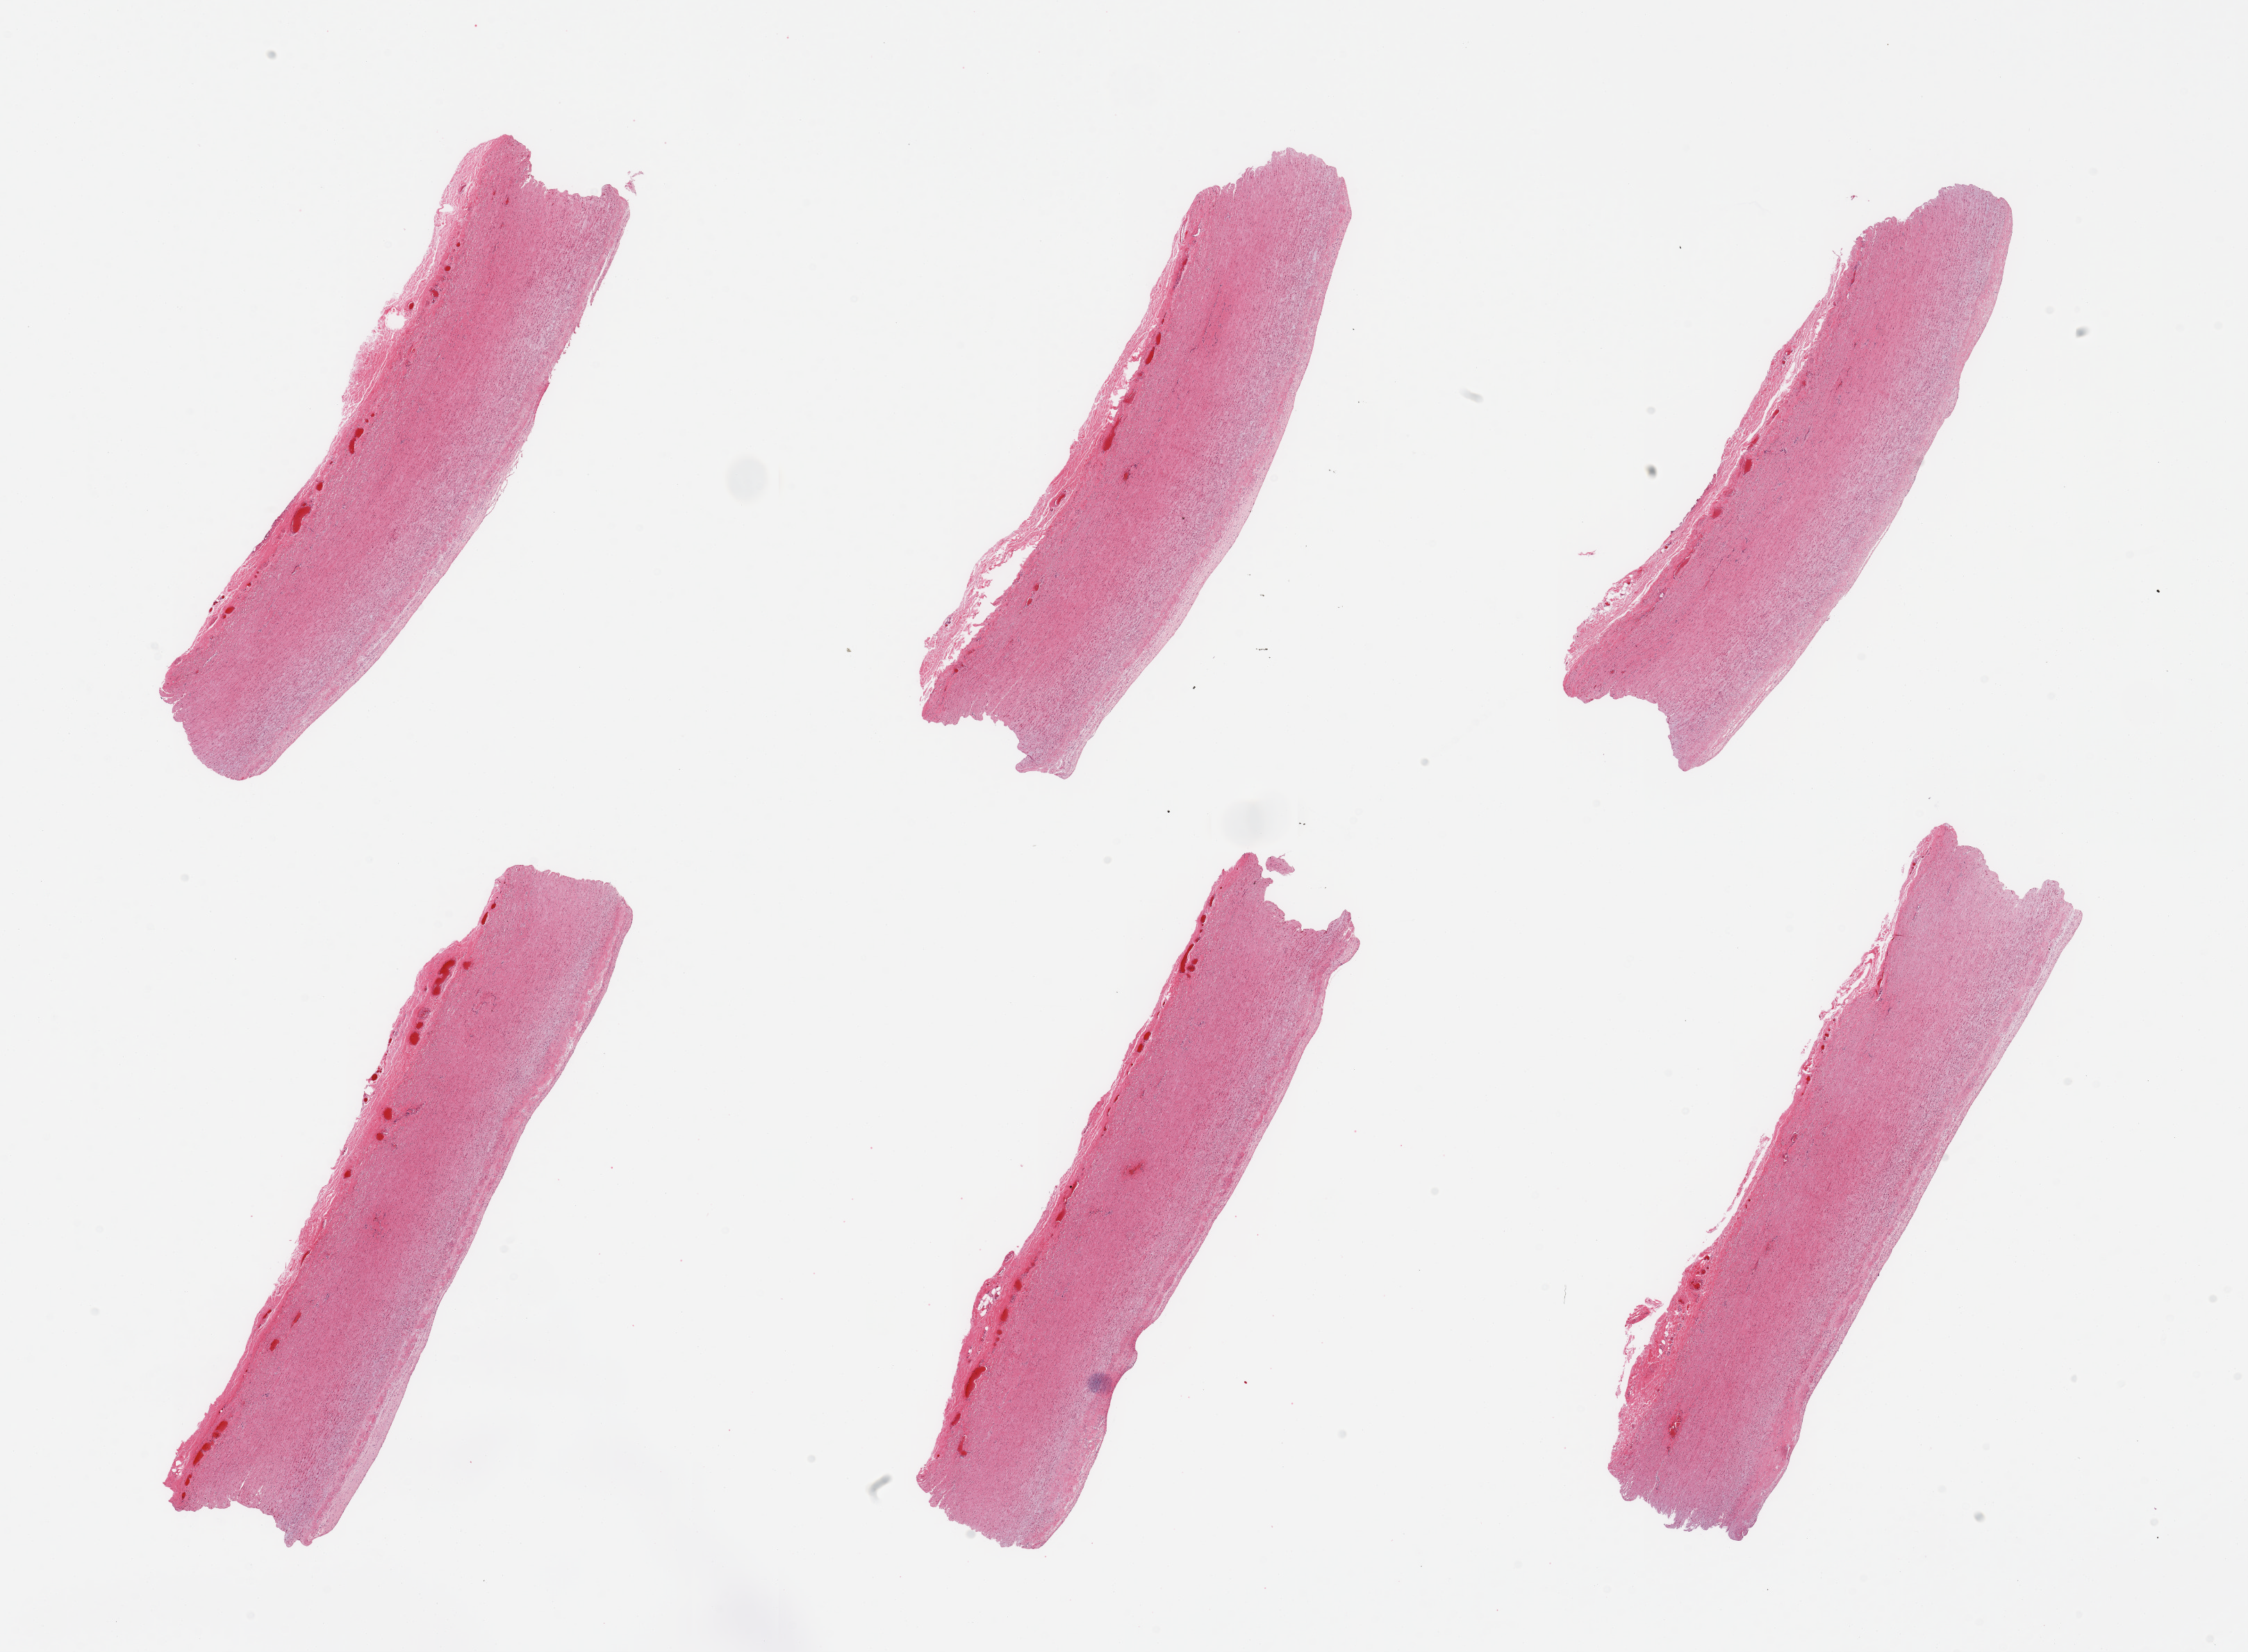
Digitized hematoxylin and eosin (H&E)-stained section, shown as a low-resolution overview of the whole scanned area (about 25.6 x 18.8 mm, from a 20x scan); PAXgene-fixed paraffin-embedded (PFPE) section; sampled site (target tissue): aorta; tissue donor sample. Donor: male.
- reviewer comment on this tissue sample: 6 pieces, minimal visible atherosis